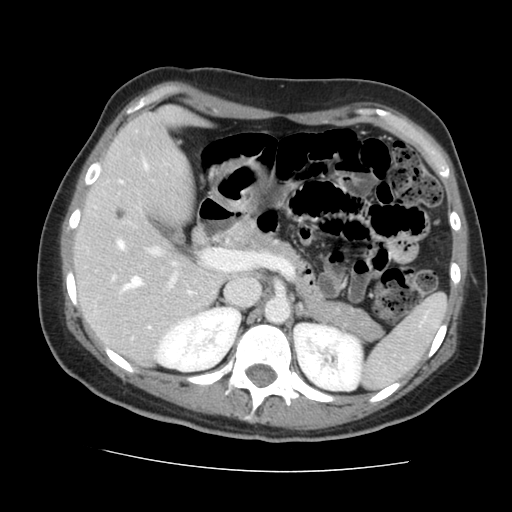
Contrast-enhanced abdominal CT, one axial slice. 120 kVp. Intravenous contrast given. Soft-tissue window (W 400 / L 40 HU). 2.5 mm slice thickness. 512 × 512 image matrix, field of view 333 × 333 mm. Female patient, age 46 years. Case-level facts recorded for this patient, not image findings: diagnosis: colorectal cancer liver metastases, imaged before liver resection; multiple liver metastases: no; largest metastasis: 2.8 cm.
Outlined on this slice (outlined manually by an expert reader):
- hepatic veins: box from (x=119, y=163) to (x=191, y=293) px
- liver: (x=77, y=110)–(x=220, y=362)
- planned liver remnant (the part of the liver to remain after resection): (x=77, y=110)–(x=220, y=362)
- portal vein (with intrahepatic branches): (x=113, y=241)–(x=226, y=287)
- liver metastasis: (x=116, y=207)–(x=127, y=221)